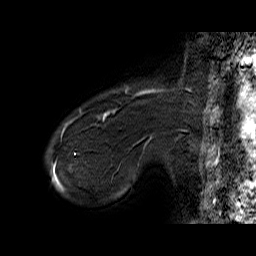
Breast MRI (dynamic contrast-enhanced), one sagittal slice; position 8 of 60 along the scan axis; dynamic contrast-enhanced series, time point 2 of 6 at this slice position (early post-contrast); 1.5 T; TE 6.4 ms, TR 32.9 ms; 4 mm slice thickness; 256 × 256 image matrix, field of view 200 × 200 mm. Female patient. Case-level facts recorded for this patient, not image findings: setting: breast cancer imaged before/during neoadjuvant chemotherapy; receptor status: HER2-positive.
Outlined on this slice (semi-automatically segmented with operator editing):
- analysis volume of interest (the breast-tissue region the enhancement analysis was run in; not a lesion): bounding box [x1, y1, x2, y2] px = [71, 81, 155, 146]
- tumour enhancement mask (voxels above the 100 % enhancement threshold inside the analysis volume of interest): [71, 90, 155, 145]